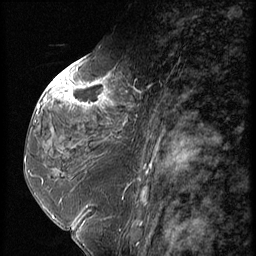
Breast MRI (dynamic contrast-enhanced), one sagittal slice. Slice 29 of 56 in the series (ordered by position). Dynamic contrast-enhanced series, image 2 of 3 at this slice position (ordered by acquisition). 1.5 T. TE 4.2 ms, TR 9 ms. 256 × 256 image matrix, field of view 180 × 180 mm. Female patient, age 59 years. Case-level facts recorded for this patient, not image findings: setting: breast cancer imaged before/during neoadjuvant chemotherapy; receptor status: HER2-positive.
Outlined on this slice (semi-automatic segmentation, software-assisted and operator-edited):
- analysis volume of interest (the breast-tissue region the enhancement analysis was run in; not a lesion): bounding box [x1, y1, x2, y2] px = [44, 66, 151, 135]
- tumour enhancement mask (voxels above the 140 % enhancement threshold inside the analysis volume of interest): [51, 75, 106, 105]